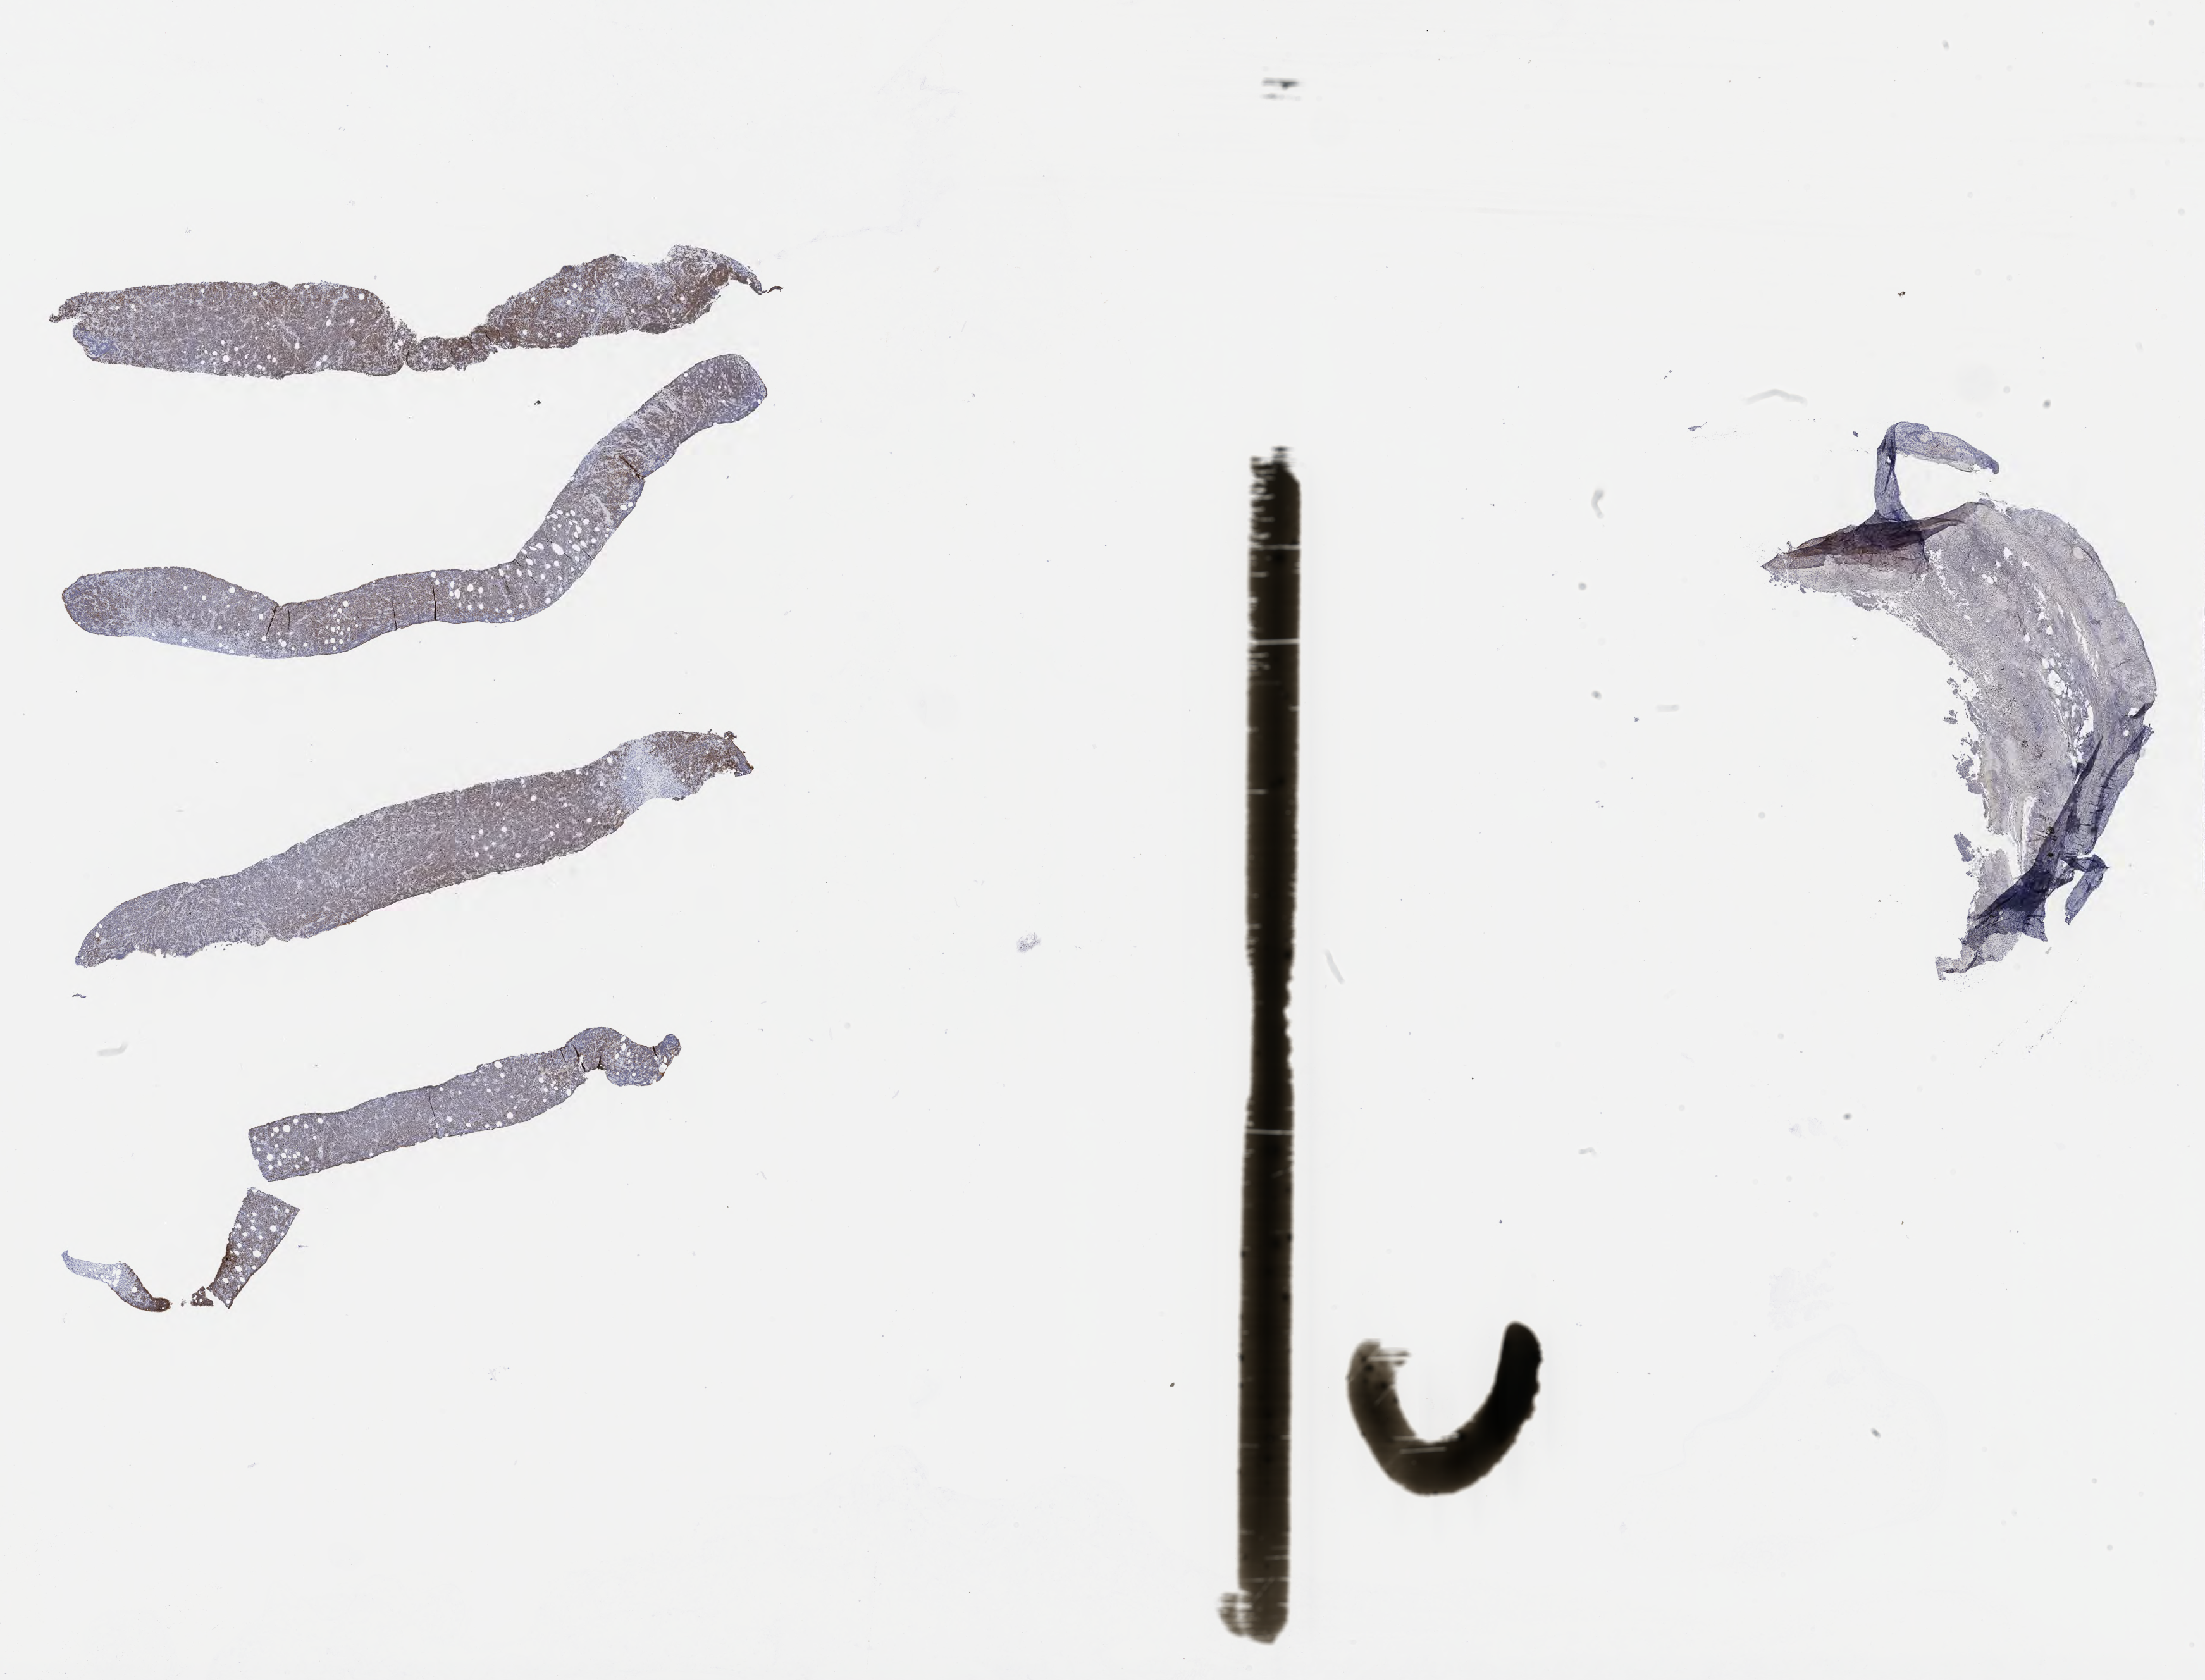
Immunohistochemistry (IHC) whole-slide image stained for Ki-67 — low-resolution overview of the scanned area, about 28.2 x 21.5 mm, tumor tissue. Patient: male, 69 years old.
Diagnosis: Diffuse large B-cell lymphoma, NOS.